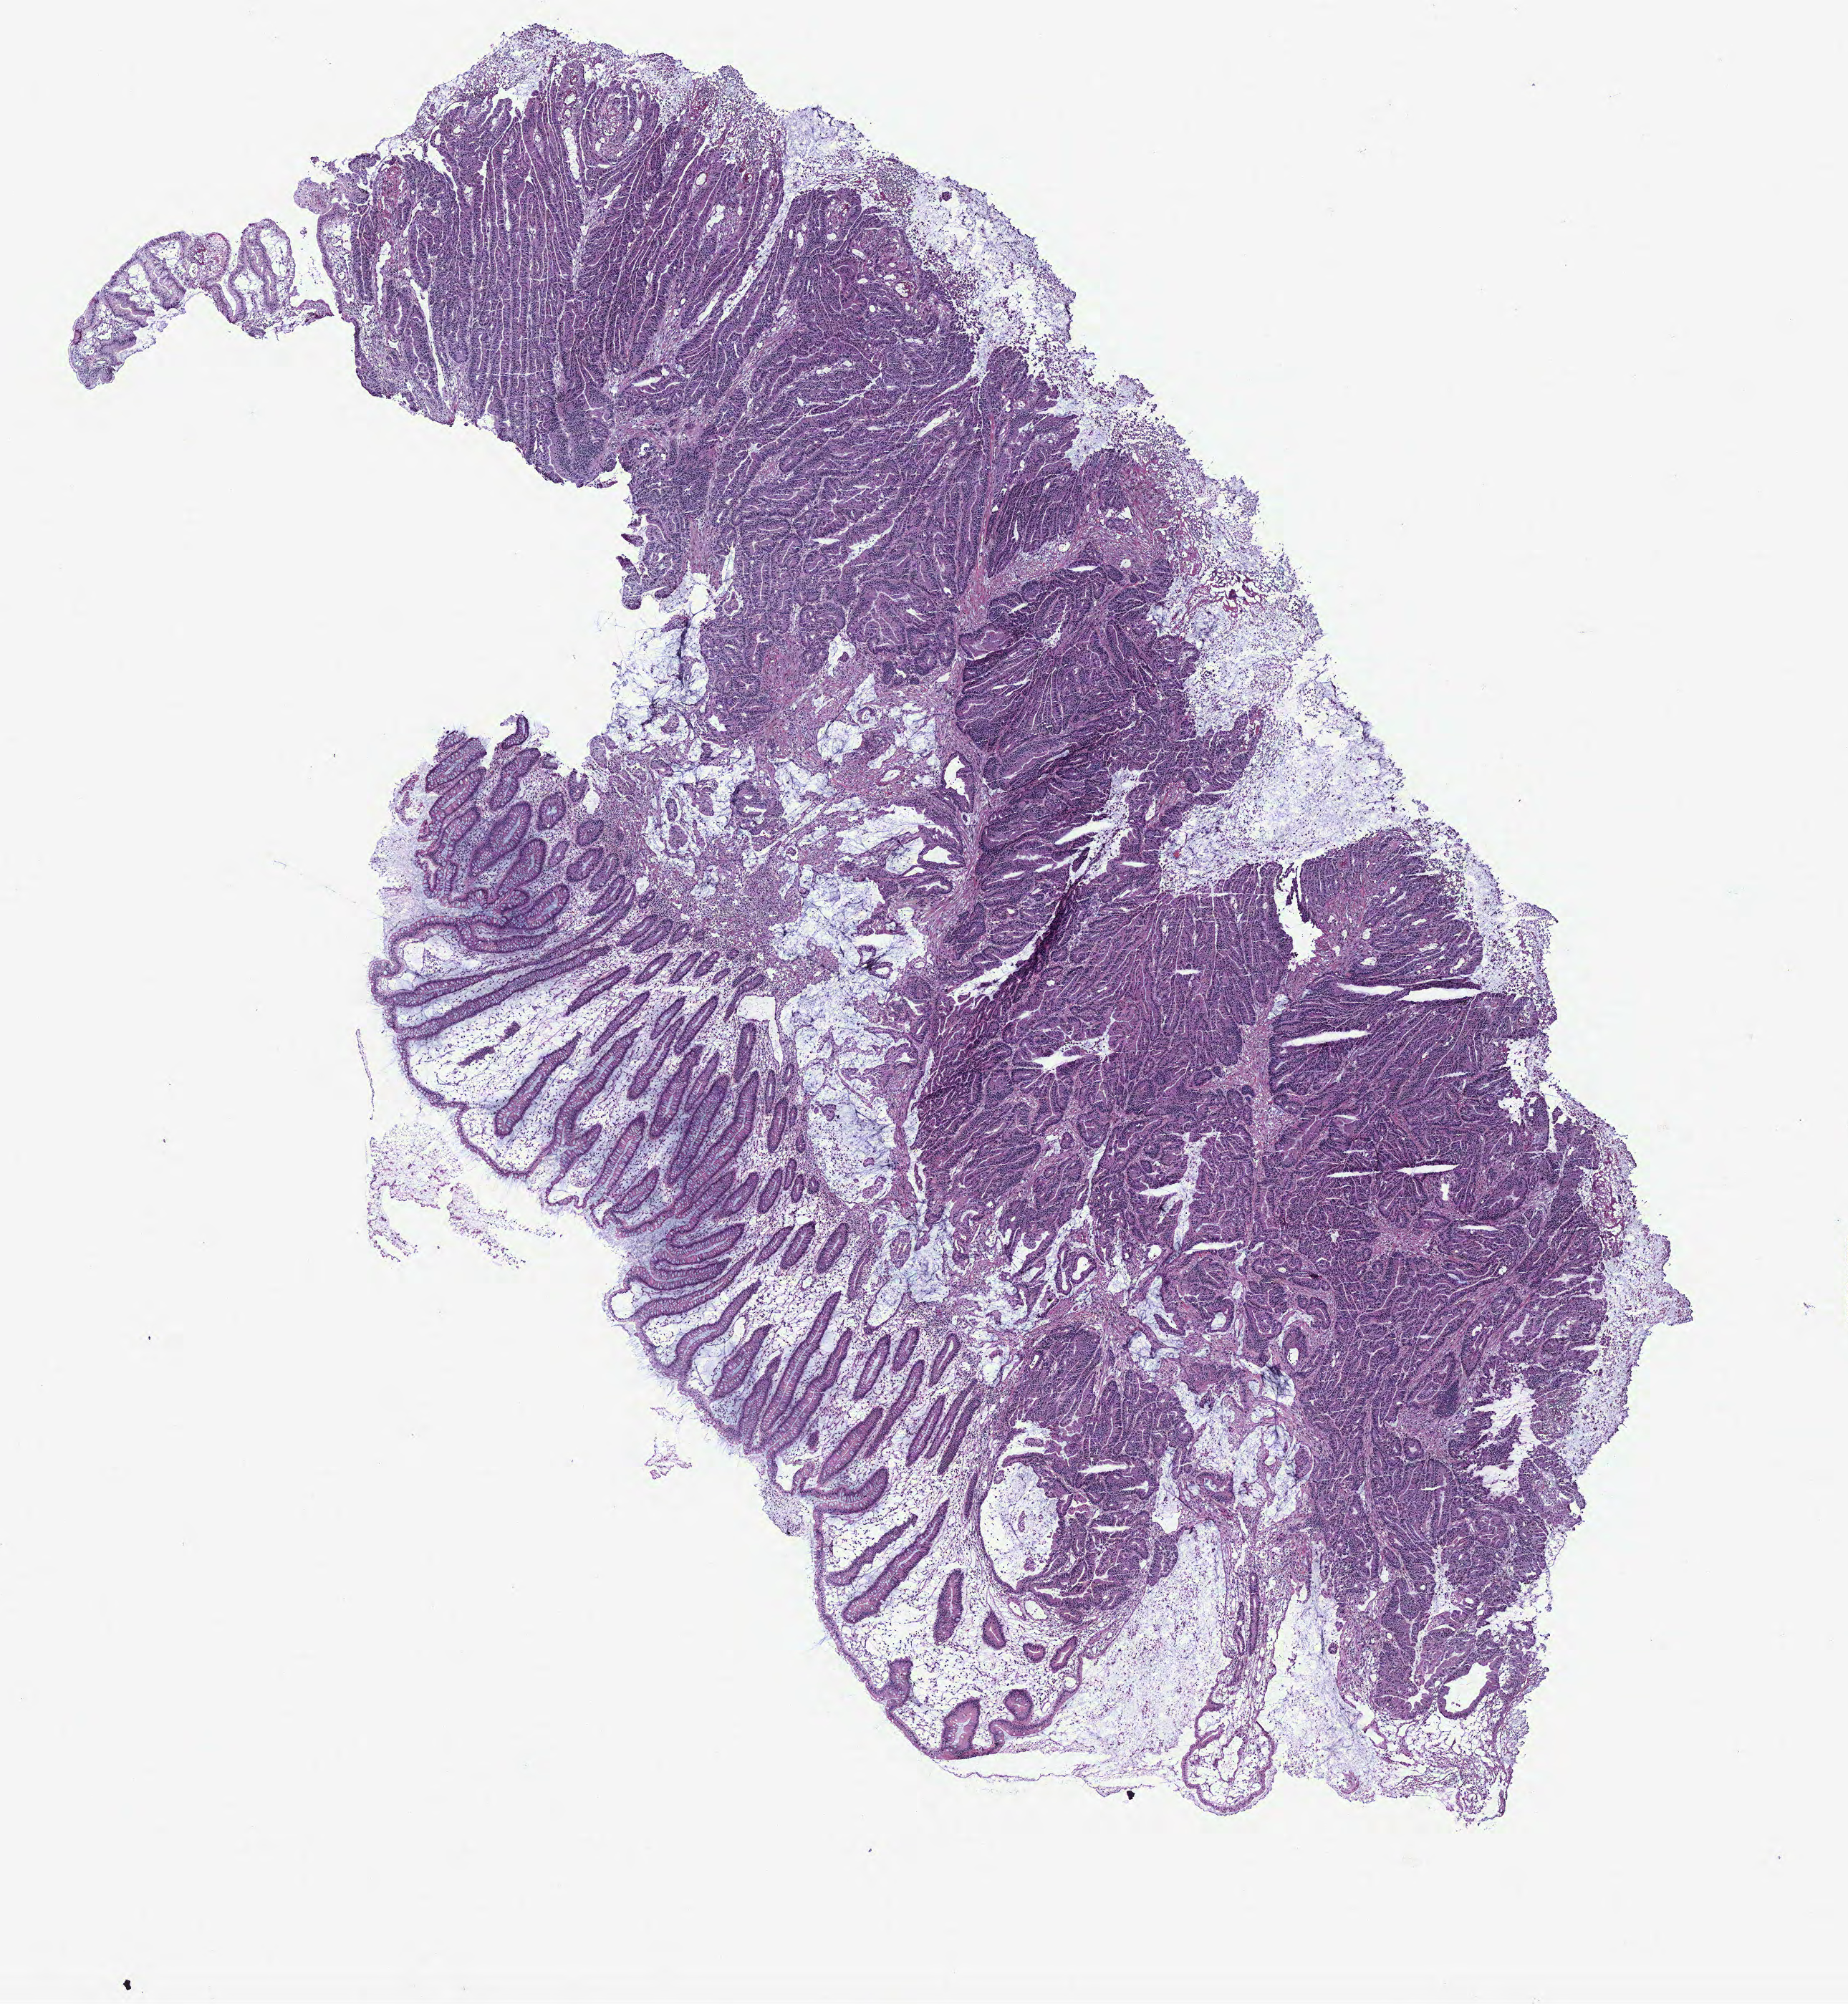
Whole-slide histology image, H&E, whole scanned area (about 10.3 x 11.2 mm, from a 40x scan) shown as a low-resolution overview; colon, normal (non-tumour) tissue. Female, 77 y/o.
• this section: normal (non-tumour) tissue from the same patient
• patient diagnosis: Adenocarcinoma, NOS